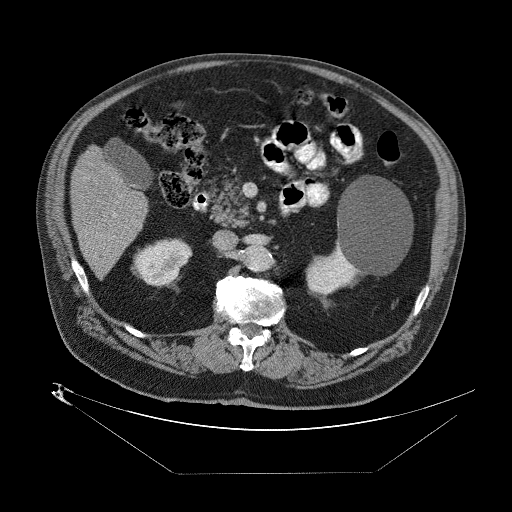
Contrast-enhanced abdominal CT (liver protocol), one axial slice. Reconstruction kernel STANDARD. 140 kVp. One of 2 acquisitions stored at this slice position. Soft-tissue window (W 400 / L 40 HU). 2.5 mm slice thickness. 512 × 512 image matrix, field of view 480 × 480 mm. From the clinical record (not read from this slice): diagnosis: hepatocellular carcinoma (patient treated with transarterial chemoembolisation; whether this scan precedes or follows treatment is not stated here); TNM stage (as recorded): Stage-II; Child-Pugh class: B; tumour differentiation: moderately differentiated; tumour nodularity: multinodular.
Outlined on this slice (semi-automatic segmentation, software-assisted and operator-edited):
- abdominal aorta: bounding box (x1, y1, x2, y2) in pixels: (246, 247, 269, 271)
- liver parenchyma outside the tumour (the mass and vessels are separate outlines, so this box may not span the whole liver): (68, 140, 148, 276)
- liver vessels: (96, 210, 117, 264)